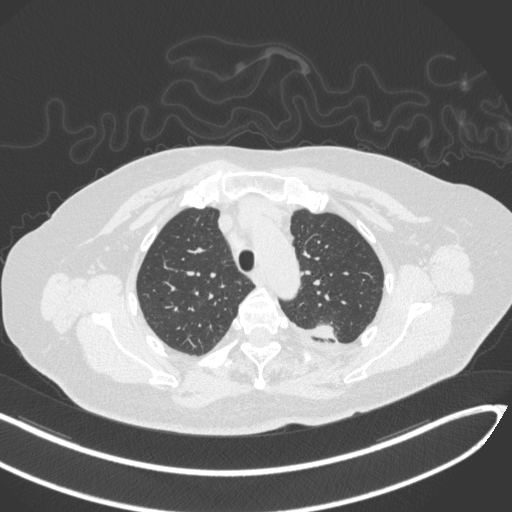
Chest CT, one axial slice; position 250 of 270 along the scan axis; reconstruction kernel B31f; lung window (W 1500 / L -600 HU); 1 mm slice thickness; 512 × 512 image matrix. Patient: female, 76 years. From the clinical record (not read from this slice): clinical TNM (as recorded): T1c N0 M0.
Structures marked on this image (rectangle marked by the reading radiologist):
- lung tumour (recorded histology: adenocarcinoma): bounding box [x1, y1, x2, y2] px = [310, 317, 340, 346]